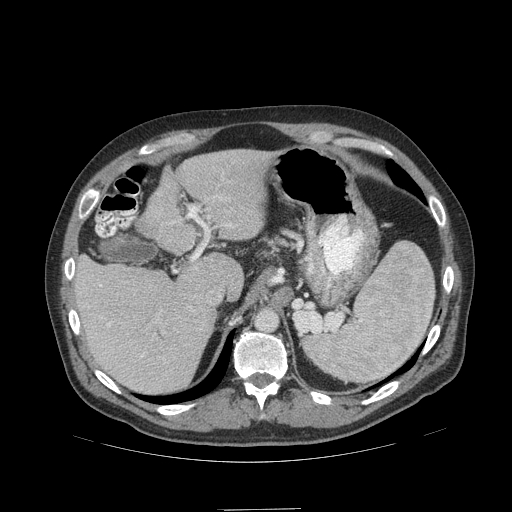
Contrast-enhanced abdominal CT (liver protocol), one axial slice; position 73 of 99 along the scan axis; reconstruction kernel STANDARD; soft-tissue window (W 400 / L 40 HU); 2.5 mm slice thickness; 512 × 512 image matrix. Case-level facts recorded for this patient, not image findings: diagnosis: hepatocellular carcinoma (patient treated with transarterial chemoembolisation; whether this scan precedes or follows treatment is not stated here); TNM stage (as recorded): Stage-I; Child-Pugh class: A; tumour differentiation: no biopsy; tumour nodularity: uninodular.
Outlined on this slice (semi-automatically segmented with operator editing):
- liver parenchyma outside the tumour (the mass and vessels are separate outlines, so this box may not span the whole liver): bounding box [x1, y1, x2, y2] px = [70, 150, 276, 392]
- liver vessels: [71, 198, 232, 358]